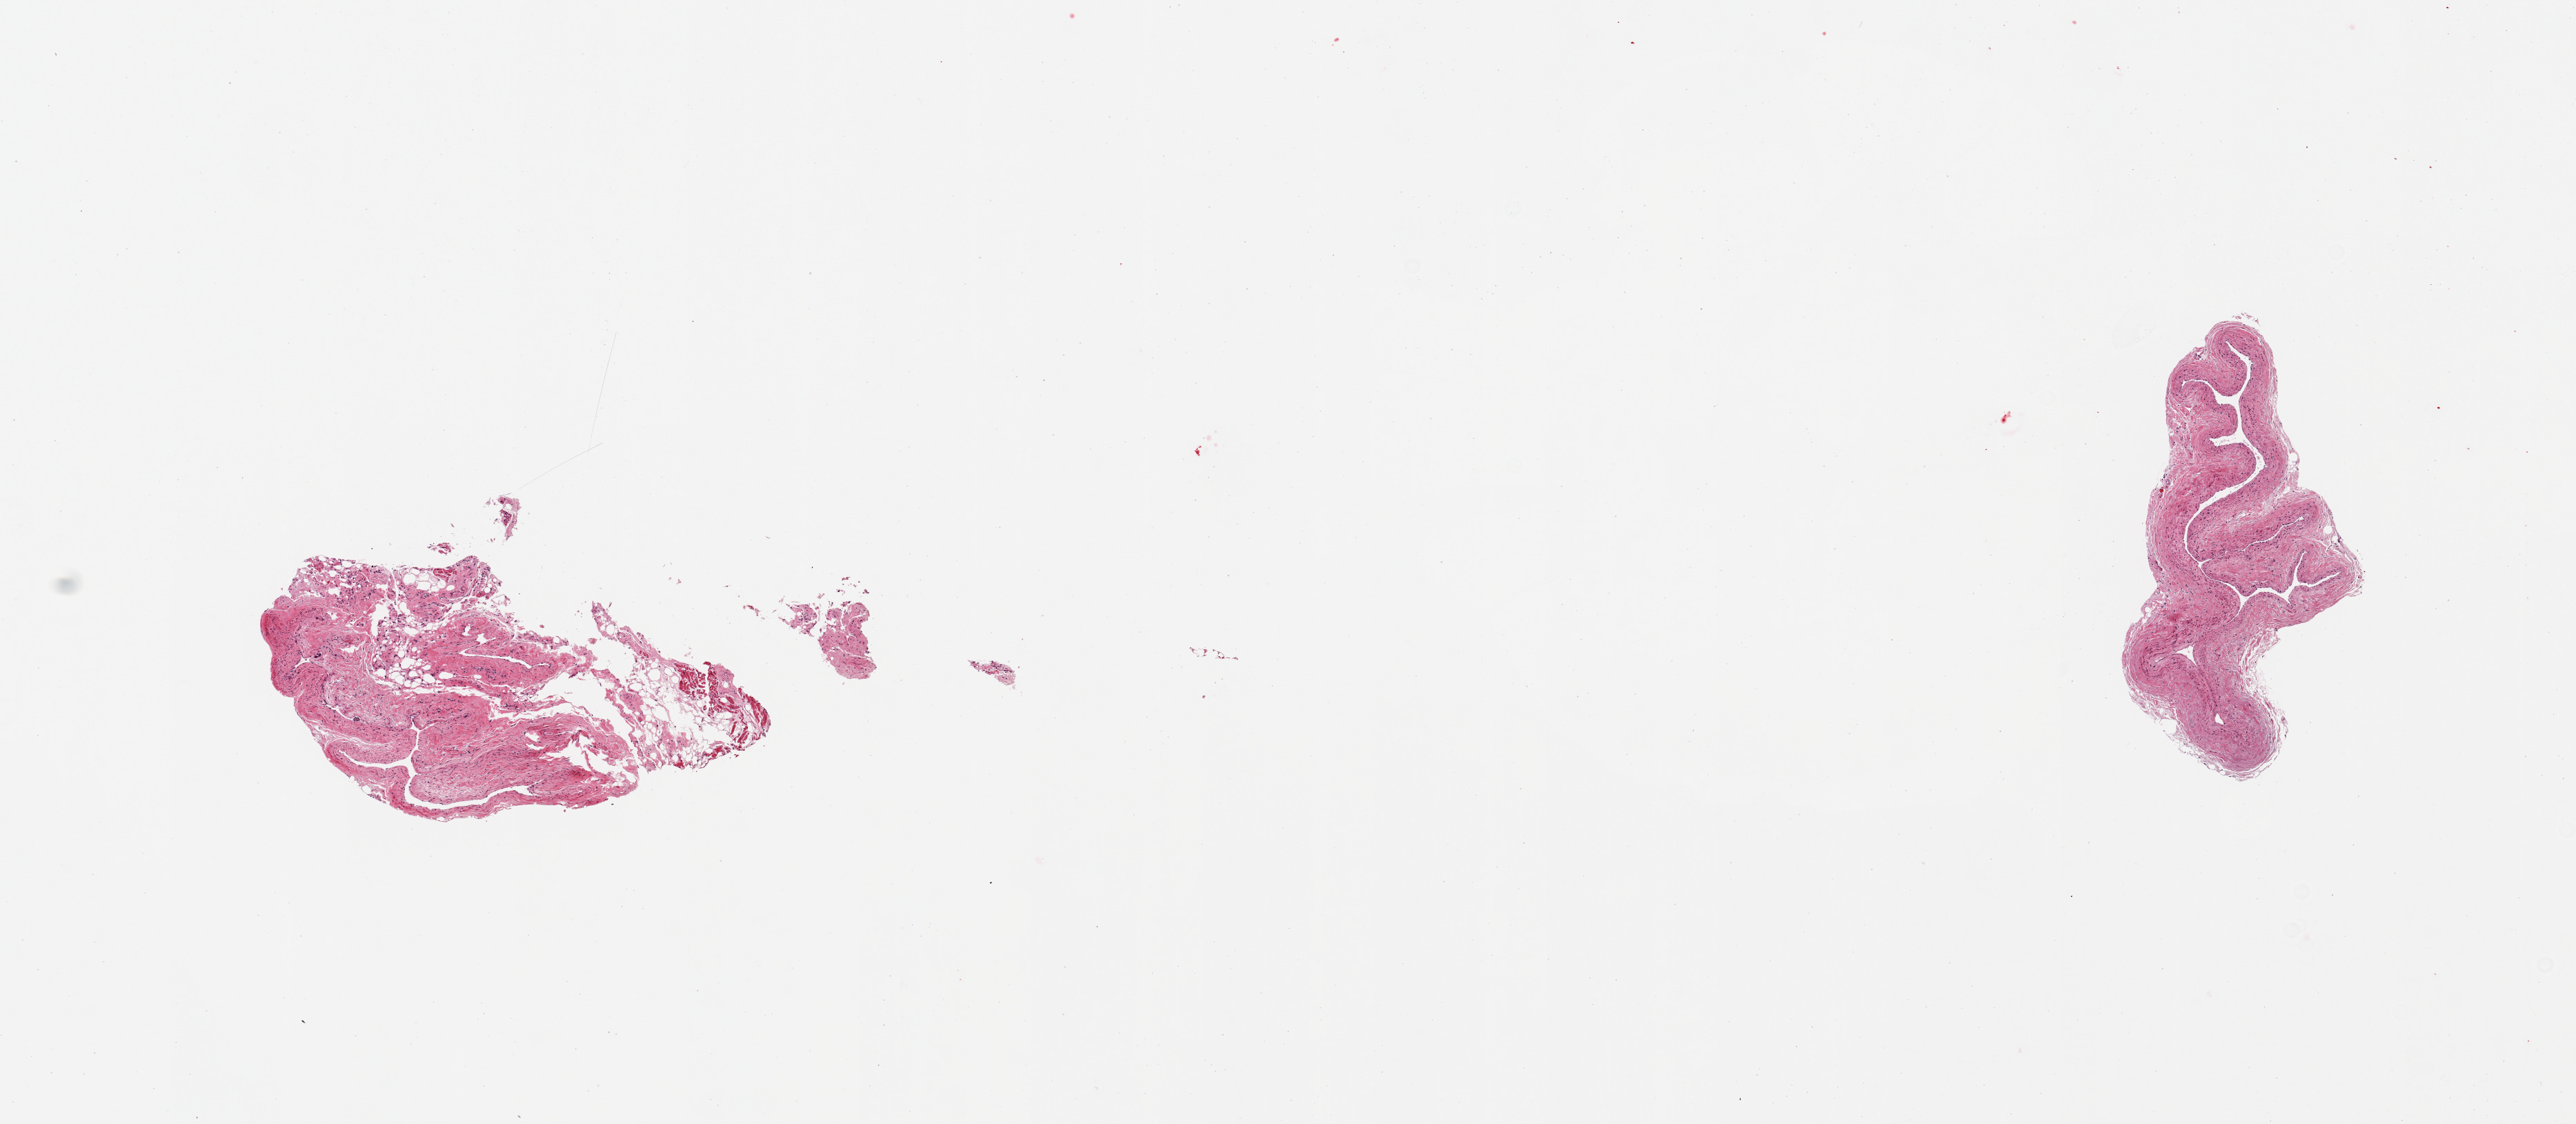
Digitized hematoxylin and eosin (H&E)-stained section, whole scanned area (about 14.8 x 6.4 mm) shown as a low-resolution overview. PAXgene-fixed, paraffin-embedded tissue. Sampled site (target tissue): coronary artery. Tissue donor sample. Female donor.
Review note (as recorded): 2 pieces; collapsed vein and fibroadipose tissue.